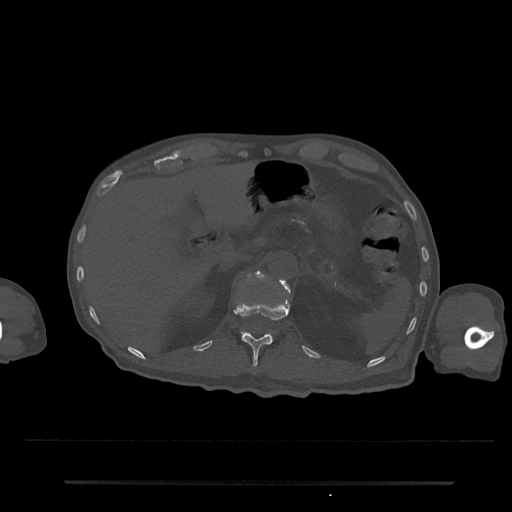
CT including the spine, one axial slice; position 179 of 797 along the scan axis; reconstruction kernel Br40s/3; 120 kVp; bone window (W 1800 / L 400 HU); 0.5 mm slice thickness; 512 × 512 image matrix, field of view 427 × 427 mm. Patient: male, 74 years. Case-level facts recorded for this patient, not image findings: primary cancer: prostate.
Outlined on this slice (semi-automatically segmented with operator editing):
- L1 vertebra: box from (x=240, y=271) to (x=290, y=336) px
- T12 vertebra: (x=234, y=301)–(x=289, y=368)